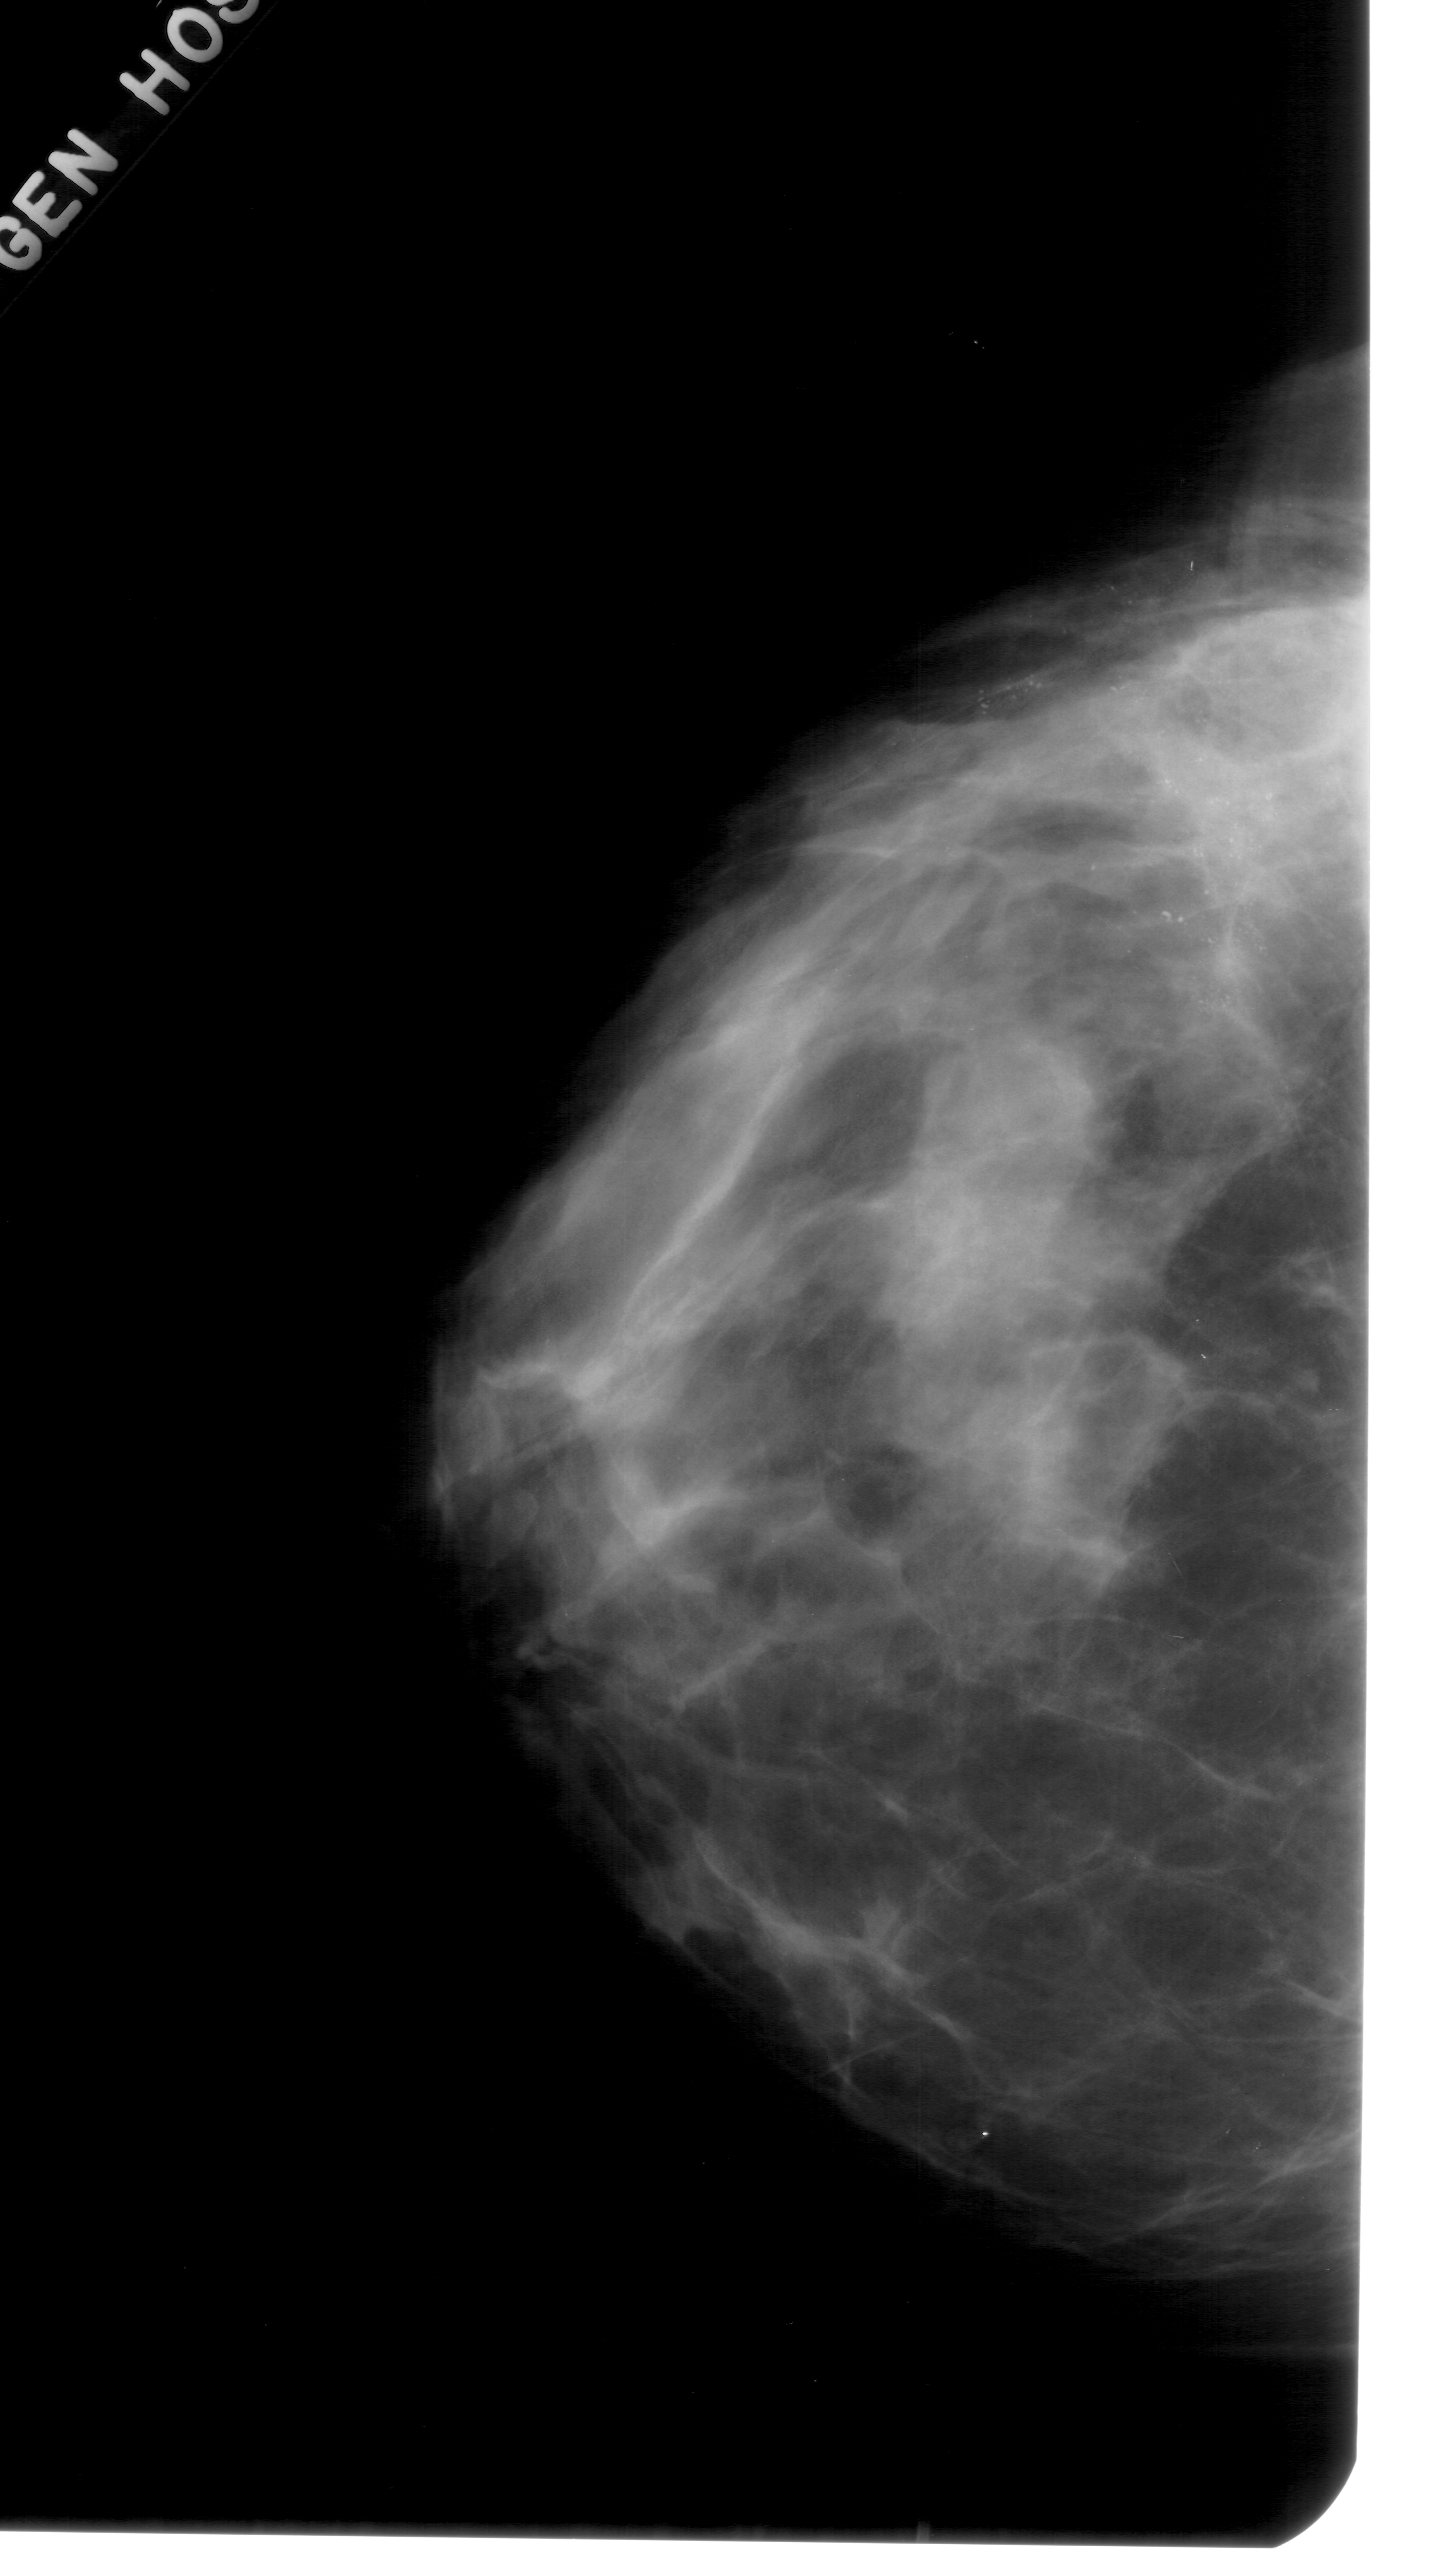
Mammogram (digitized film), left breast, craniocaudal (CC) view, BI-RADS breast density category 4 (scale 1–4).
Marked abnormality: calcifications, morphology pleomorphic, distribution segmental; BI-RADS assessment category 5; subtlety rating 4 on a 1 (subtle) to 5 (obvious) scale; pathology (as recorded): malignant.